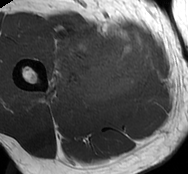
MRI of an extremity soft-tissue mass, one axial slice. MR volume resampled by the dataset authors to the PET/CT grid (not the native acquisition matrix). 188 × 174 image matrix, field of view 184 × 170 mm. Male patient. Case-level facts recorded for this patient, not image findings: histological type: undifferentiated - pleiomorphic; grade: high; site of the primary tumour: right thigh.
Outlined on this slice (expert contour drawn on MRI and transferred to this co-registered scan by the dataset authors):
- gross tumour volume including surrounding oedema: box from (x=47, y=26) to (x=153, y=104) px
- gross tumour volume (mass): (x=77, y=33)–(x=153, y=102)